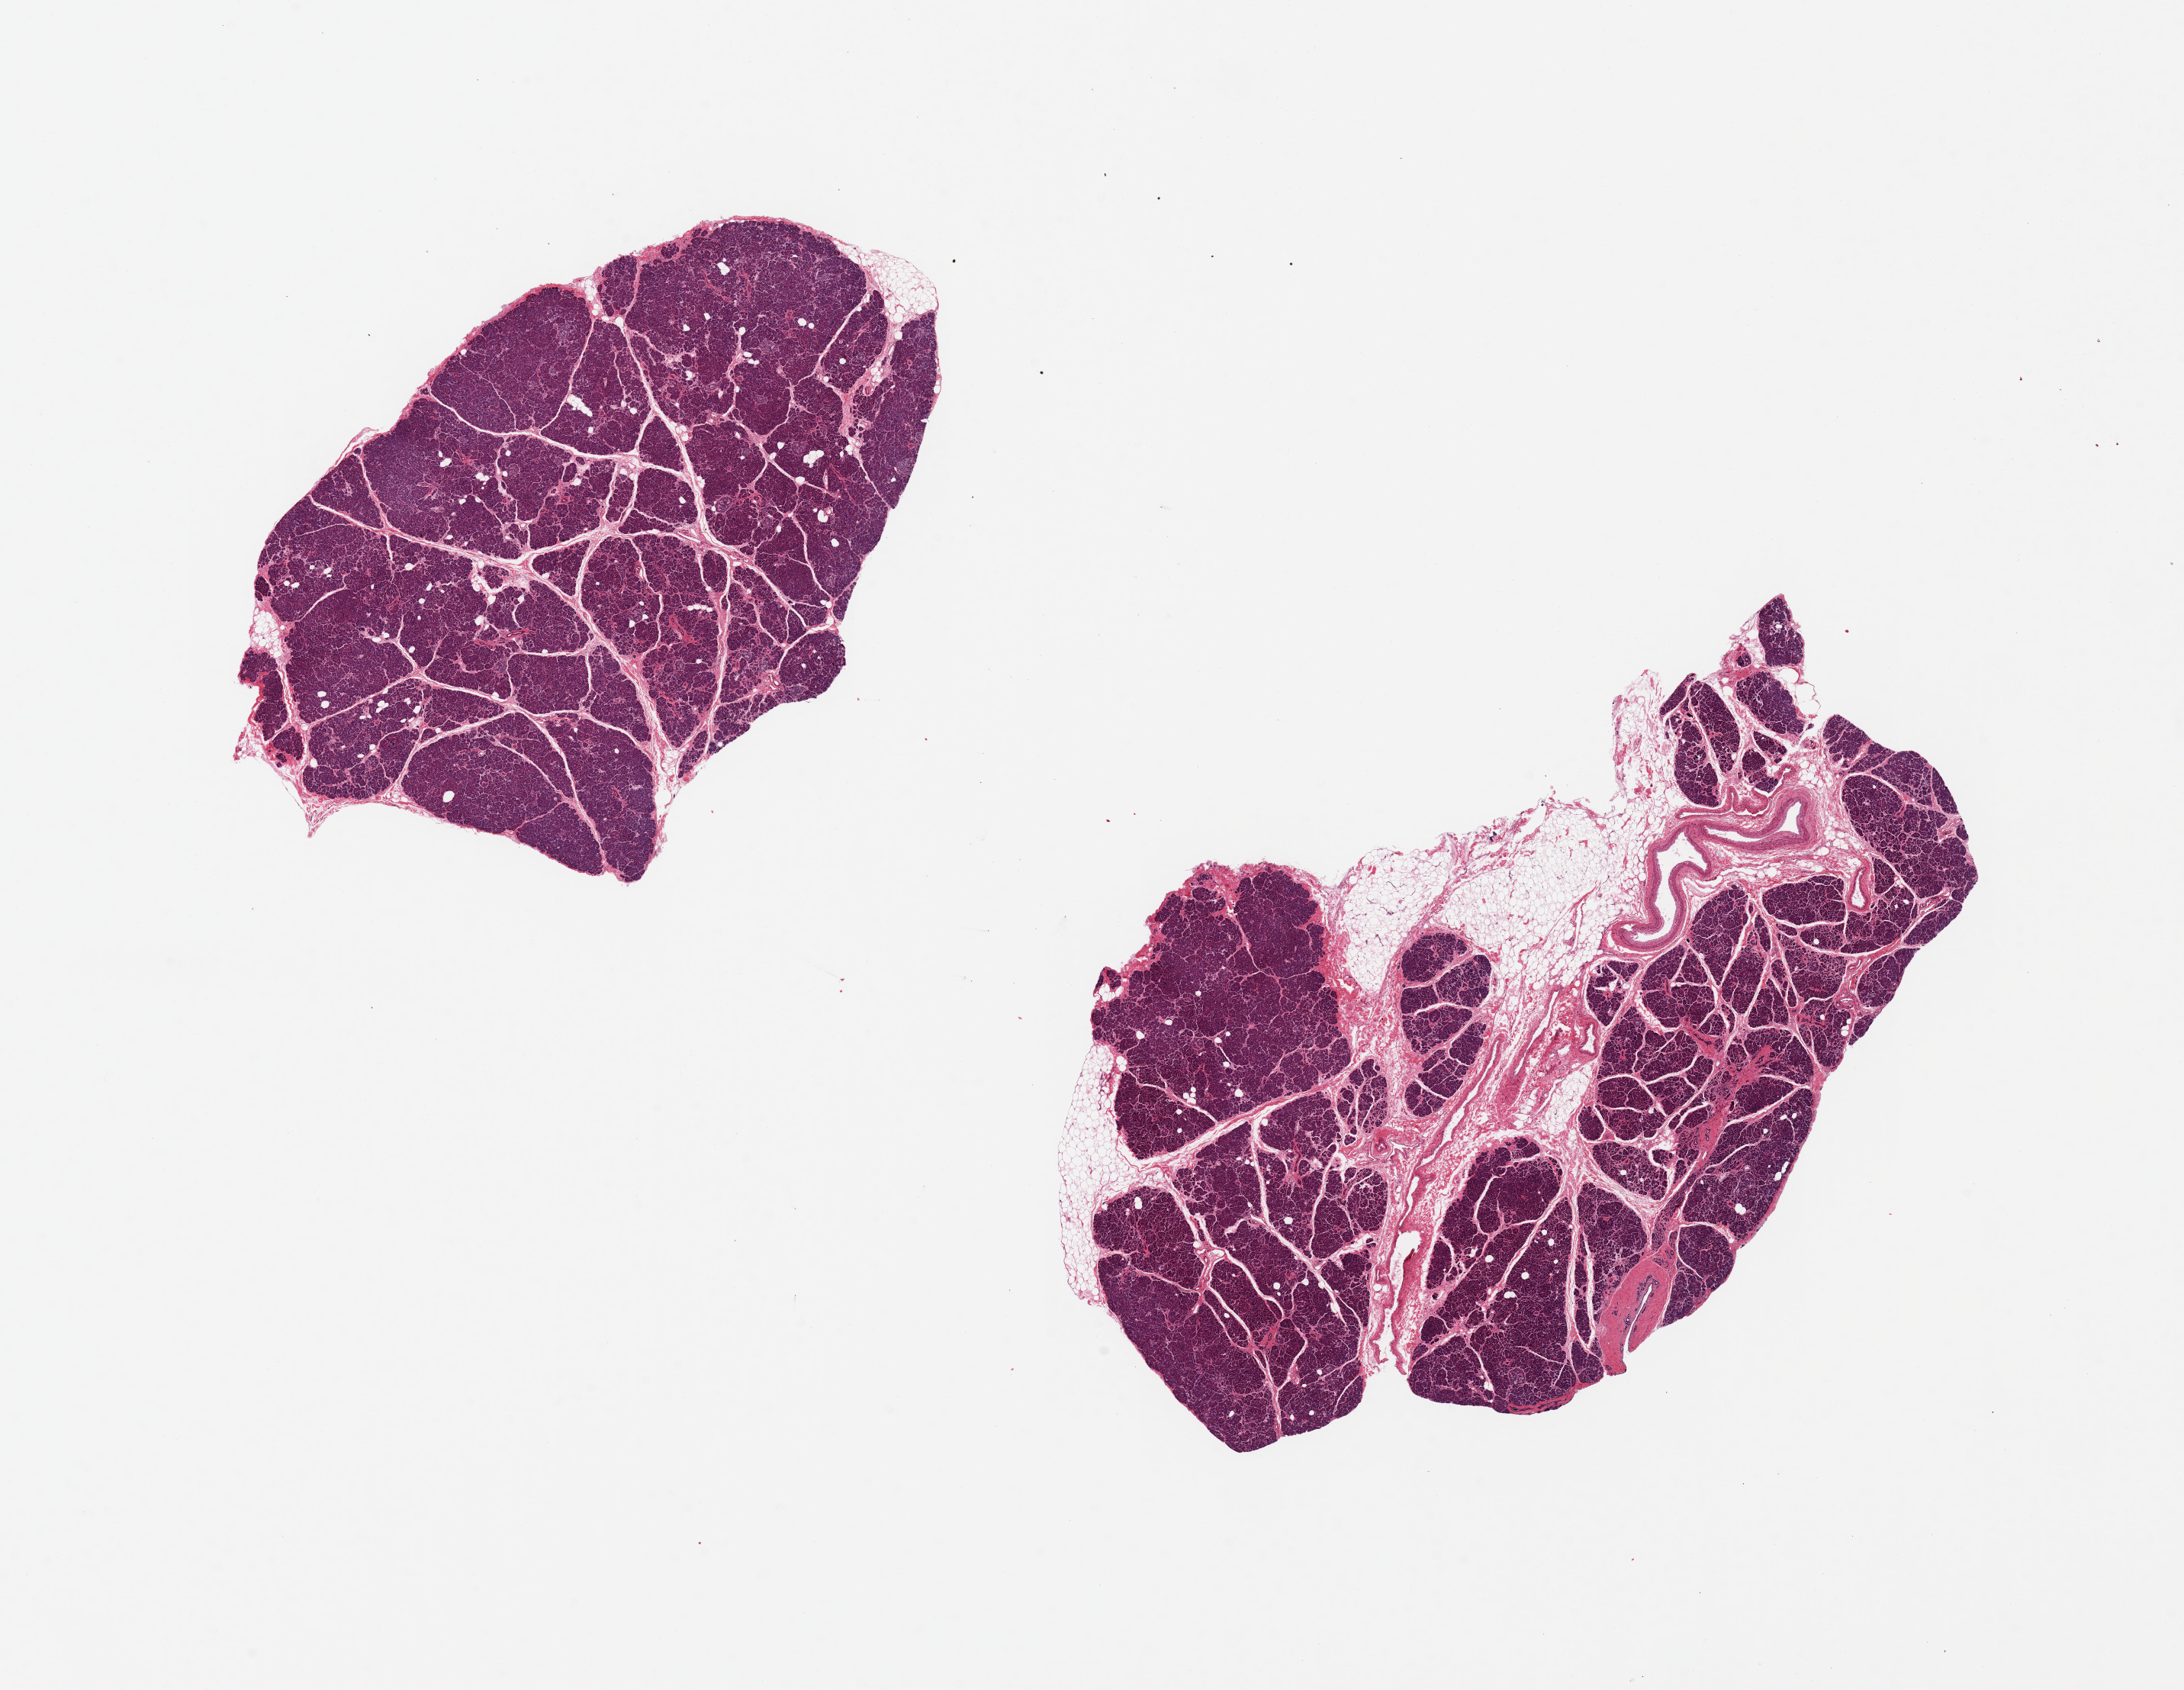
Digitized haematoxylin and eosin-stained section, brightfield, shown as a low-resolution overview of the whole scanned area (about 22.6 x 17.5 mm, acquisition: 20x scan); PAXgene-fixed paraffin-embedded (PFPE) section; sampled site (target tissue): pancreas; tissue donor sample. Female donor.
Pathologist's review note for this sample: 2 pieces 7x5 & 10x6 mm; good acinar and islet preservation; one piece has ~20% adipose.